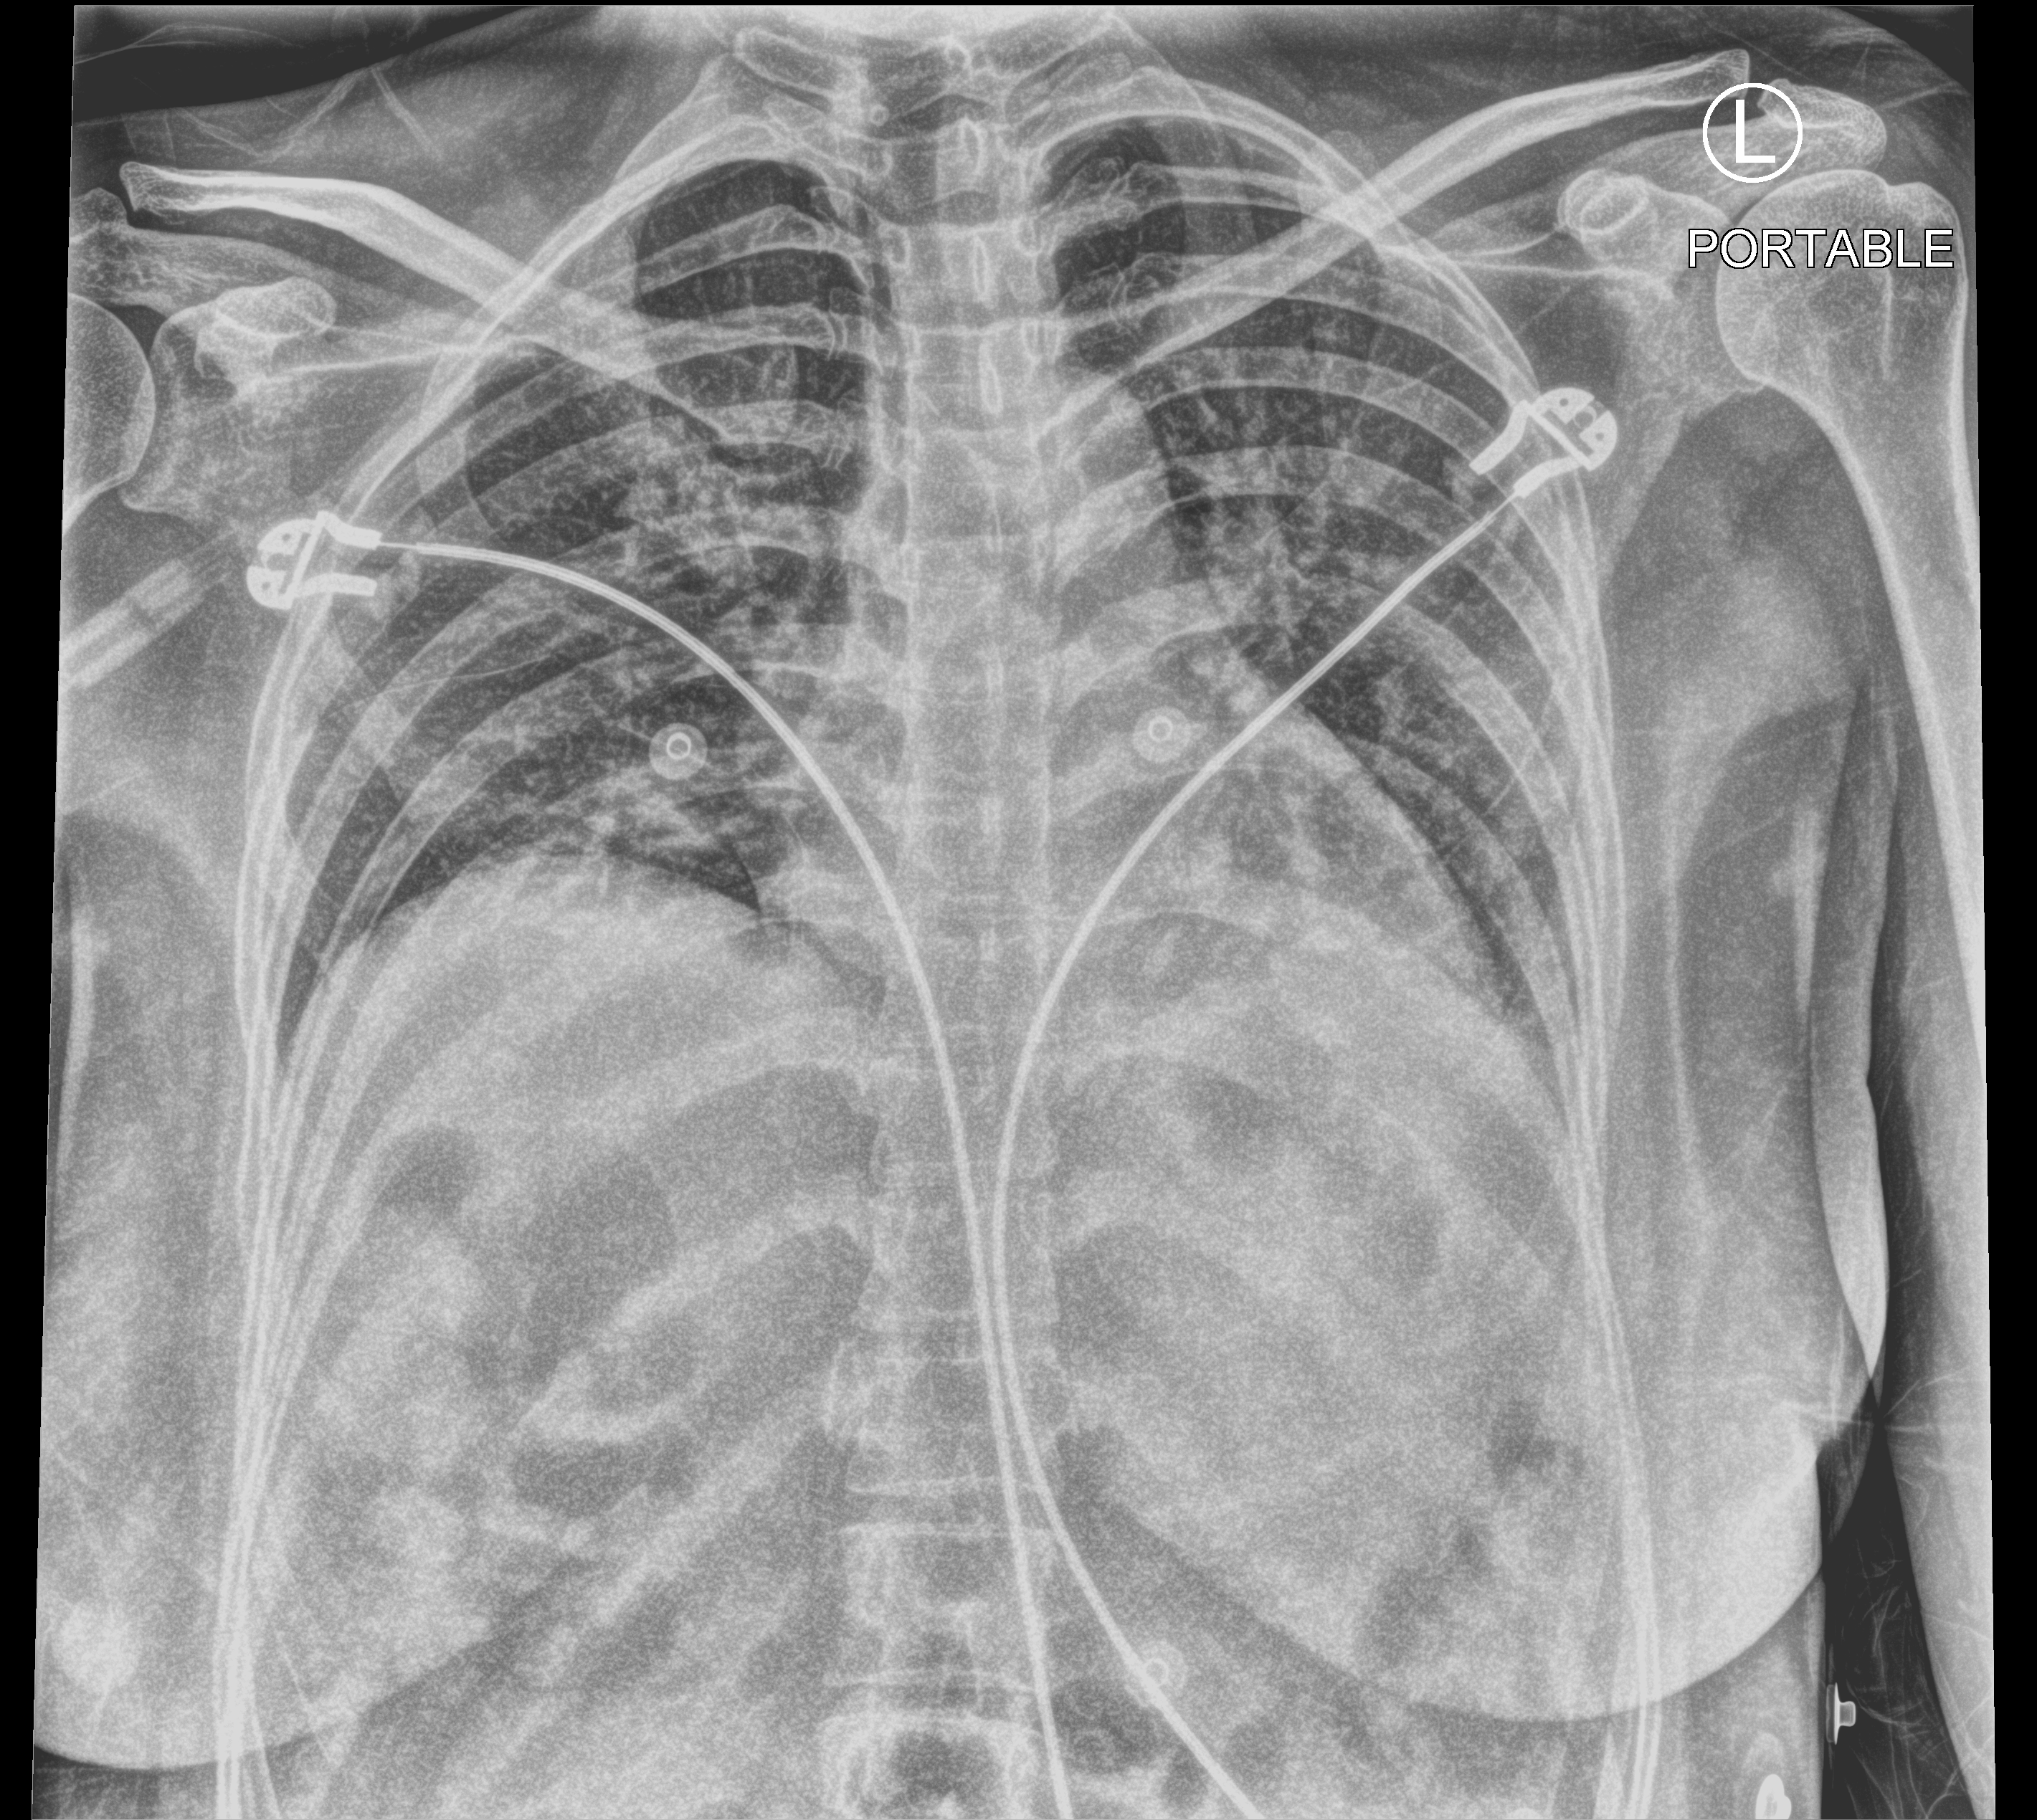
Portable chest radiograph, anteroposterior (AP) projection. Patient hospitalised with COVID-19; female, aged 18–59 years.
Admission-level facts for this patient (not findings on this image; timing relative to this image not recorded): mechanically ventilated during this hospital stay: no; COPD (admission record): no; admitted to intensive care during this hospital stay: no.